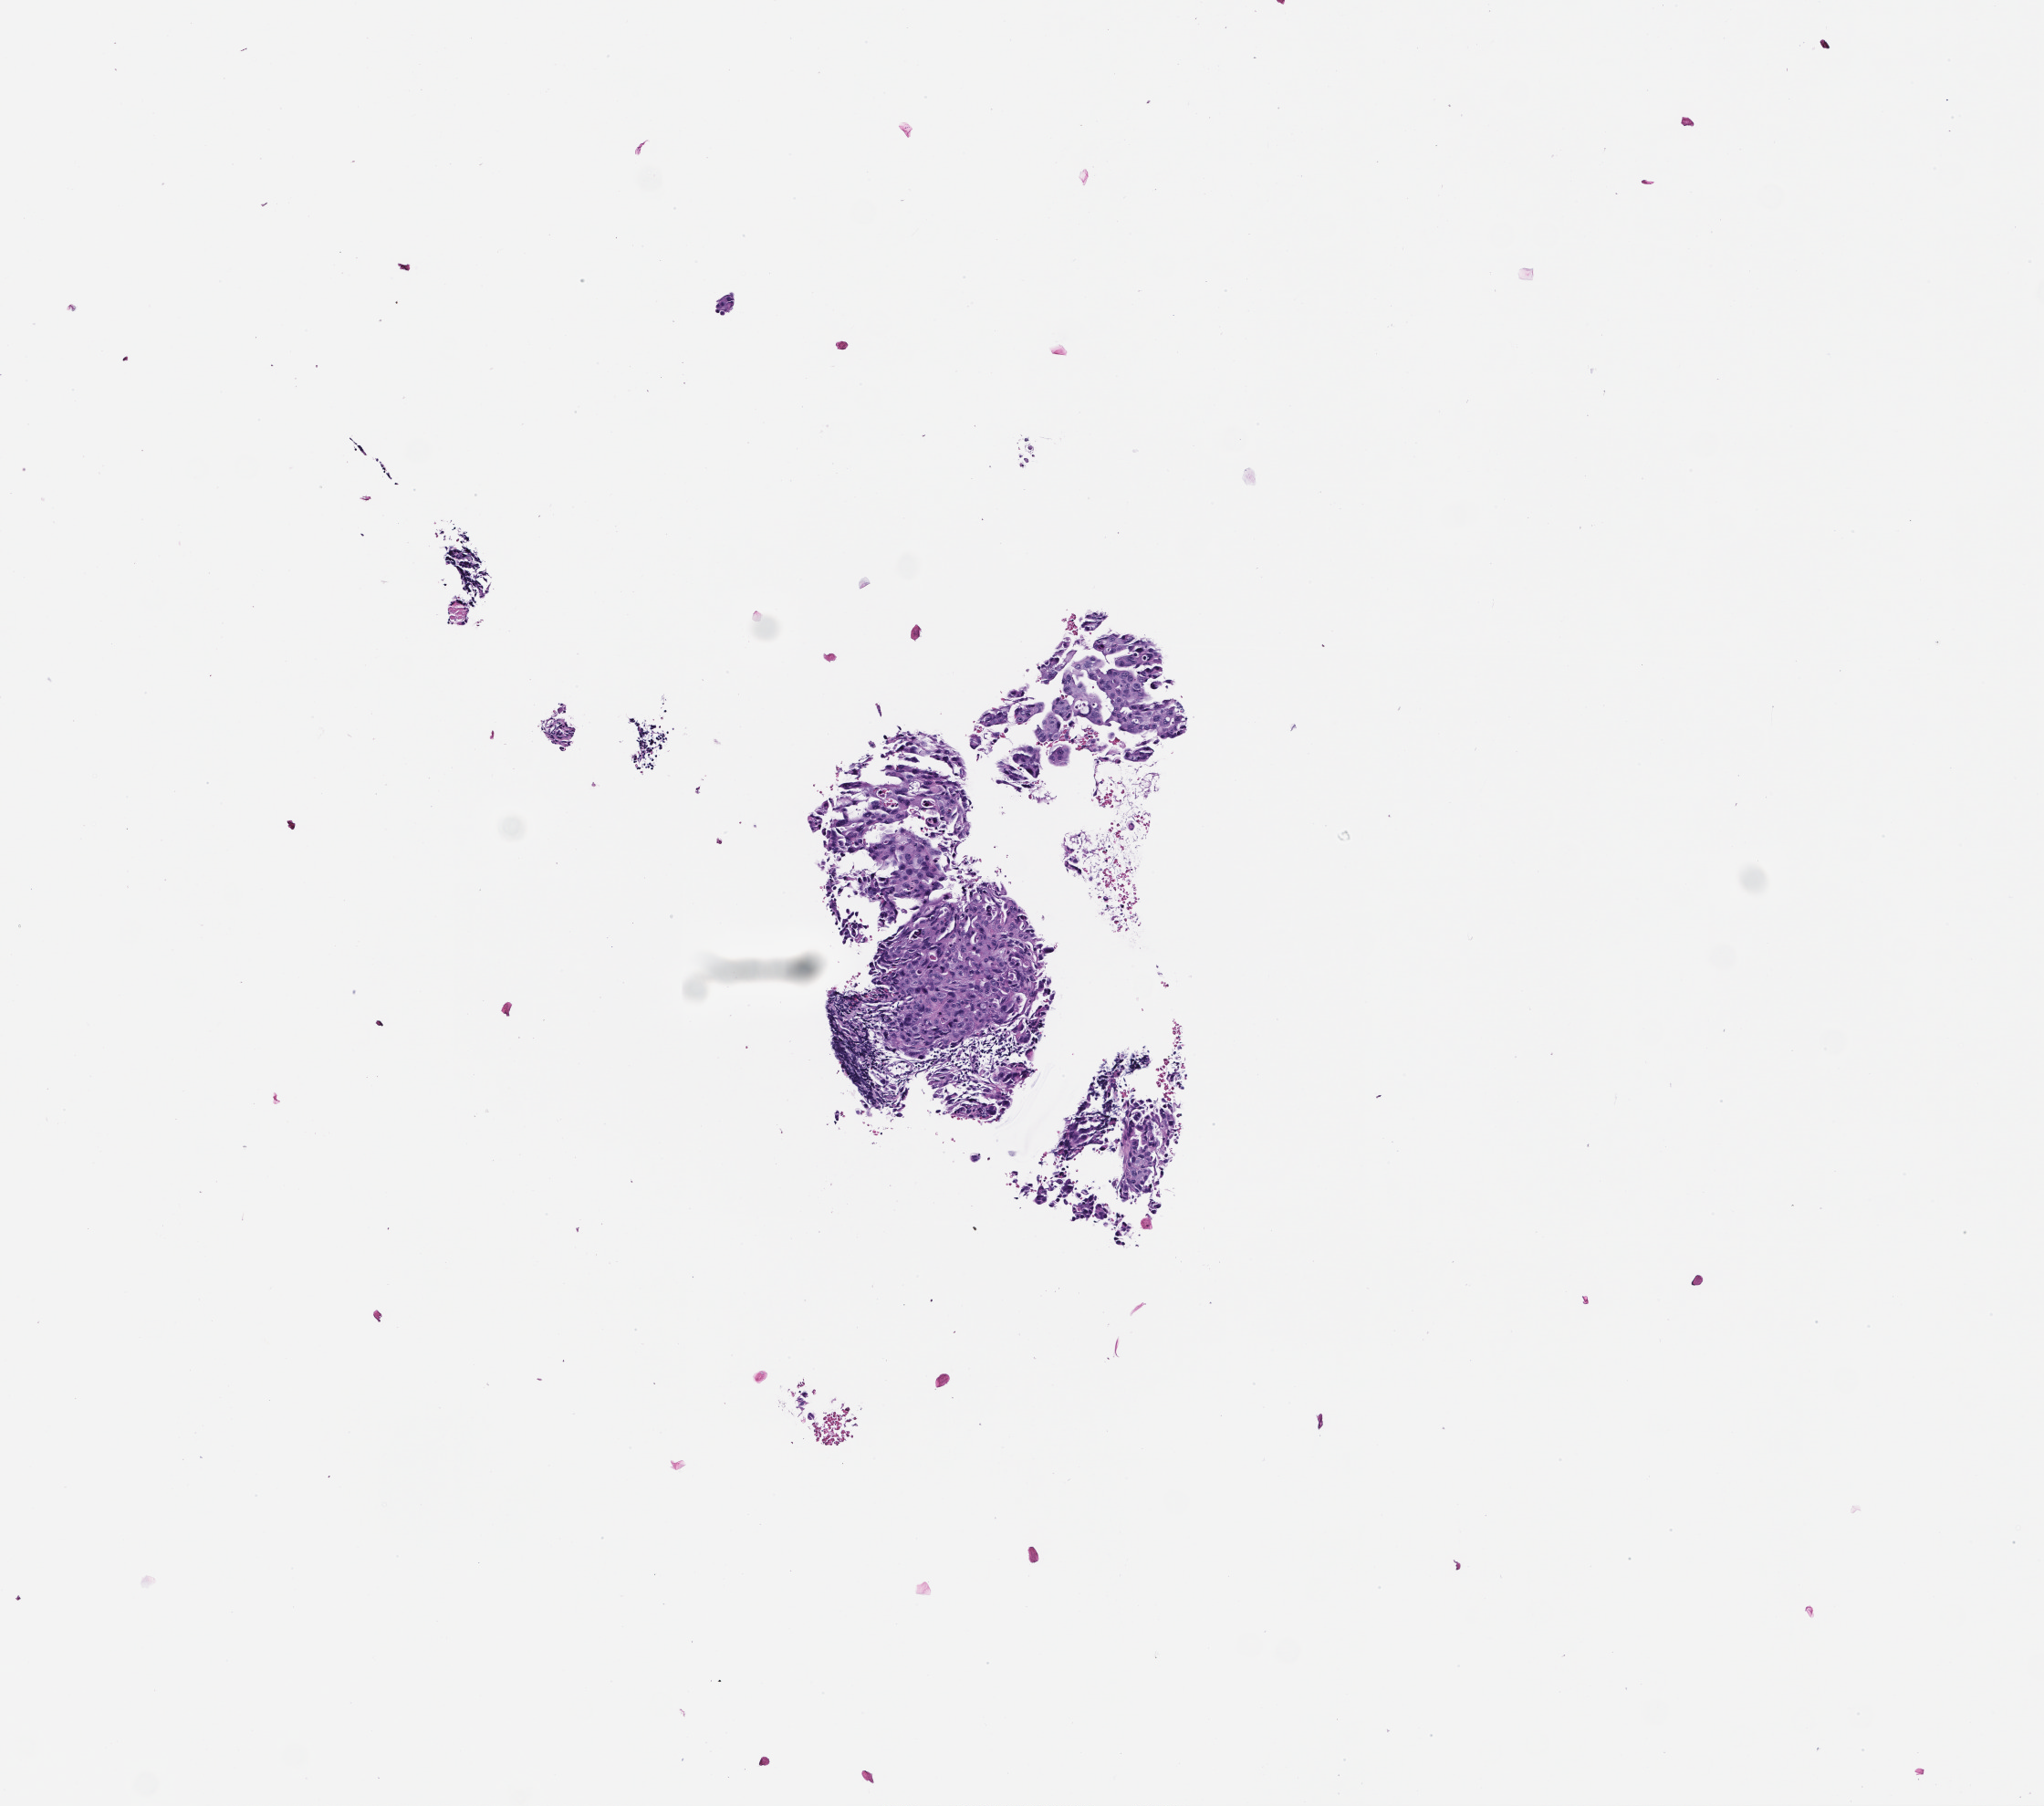
Digitized hematoxylin and eosin (H&E)-stained section — whole scanned area (about 4.5 x 4.0 mm) shown as a low-resolution overview, formalin-fixed, paraffin-embedded (FFPE) tissue, collected at baseline (before treatment). Patient sex: female.
This section: metastasis (sampled organ not recorded). Patient diagnosis (primary): Small Cell Lung Carcinoma.